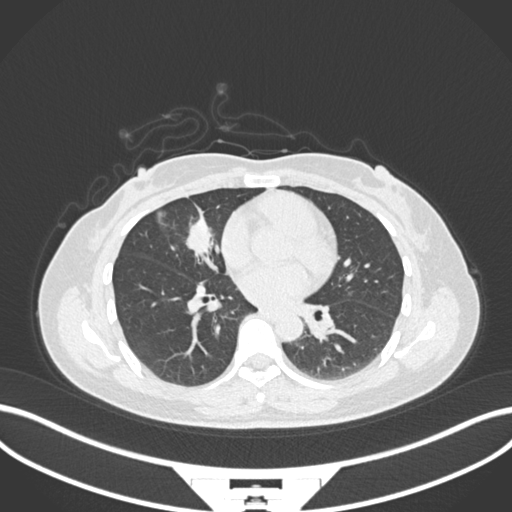
Chest CT, one axial slice; position 78 of 171 along the scan axis; lung window (W 1500 / L -600 HU); 512 × 512 image matrix, field of view 400 × 400 mm. Patient: female, 43 years. Case-level facts recorded for this patient, not image findings: clinical TNM (as recorded): T1c N3 M1; histopathological grade: G1.
Outlined on this slice (rectangle marked by the reading radiologist):
- lung tumour (recorded histology: adenocarcinoma): bounding box (x1, y1, x2, y2) in pixels: (186, 211, 217, 267)